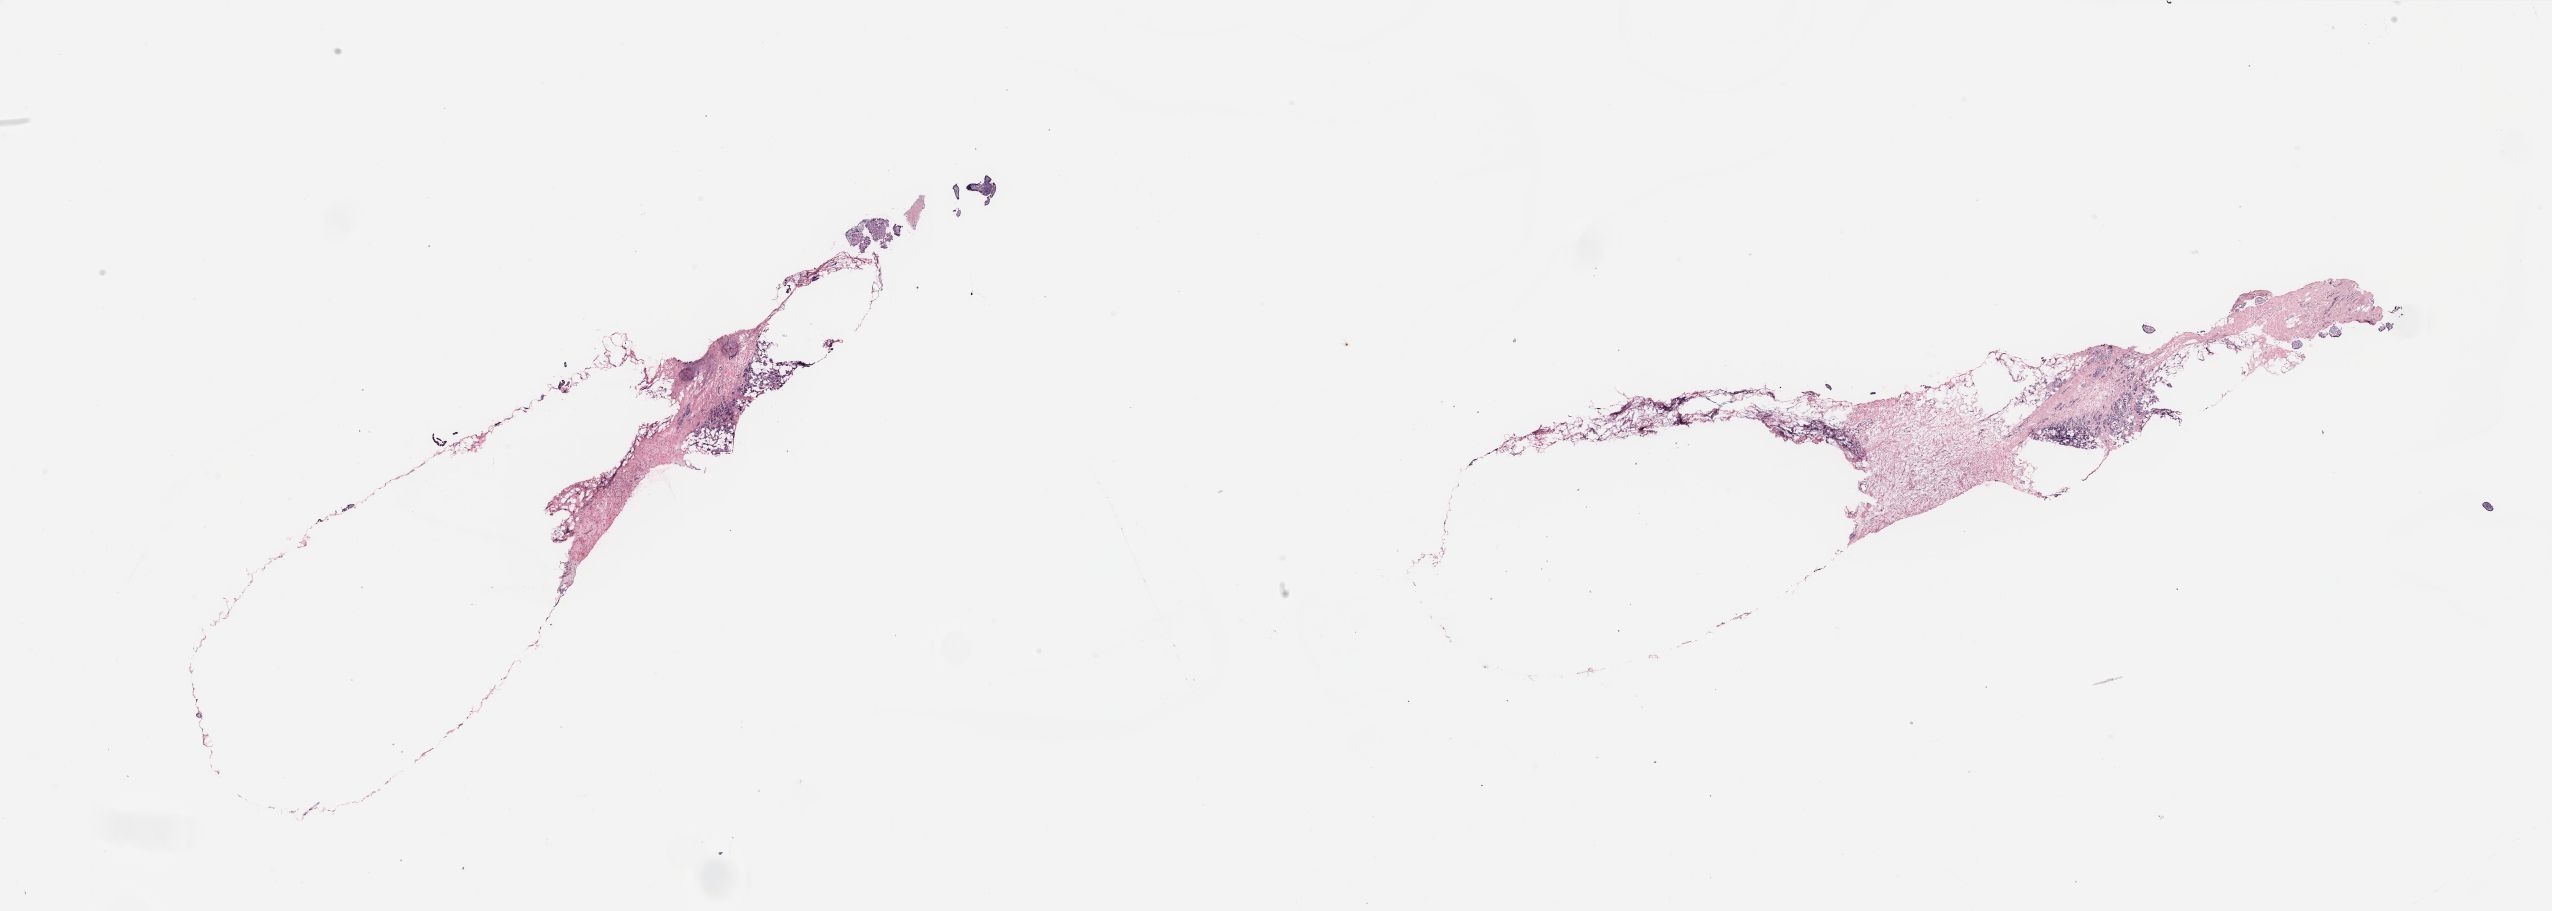
Digitized Hematoxylin and eosin (H&E) stained tissue section (whole slide) — whole scanned area (about 40.4 x 14.4 mm) shown as a low-resolution overview; tumour tissue sample, breast. Patient: female, age 62 years.
Histologic diagnosis: Infiltrating duct carcinoma, NOS.